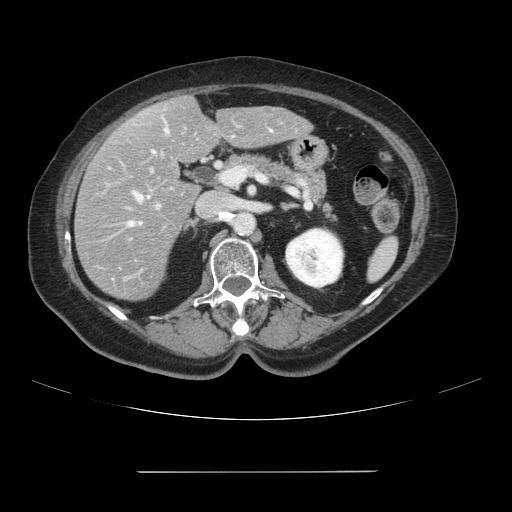
Contrast-enhanced abdominal CT, one axial slice; slice 47 of 111 in the series (ordered by position); 120 kVp; soft-tissue window (W 400 / L 40 HU); 2.5 mm slice thickness; 512 × 512 image matrix, field of view 400 × 400 mm. Female patient, age 74 years. From the clinical record (not read from this slice): diagnosis: colorectal cancer liver metastases, imaged before liver resection; multiple liver metastases: yes; largest metastasis: 1.1 cm; disease in both lobes: yes.
Annotated regions visible in this slice (expert manual segmentation):
- hepatic veins: bounding box [x1, y1, x2, y2] px = [128, 130, 168, 226]
- liver: [75, 96, 311, 301]
- planned liver remnant (the part of the liver to remain after resection): [142, 97, 311, 164]
- portal vein (with intrahepatic branches): [156, 205, 160, 209]
- liver metastasis: [262, 106, 271, 116]